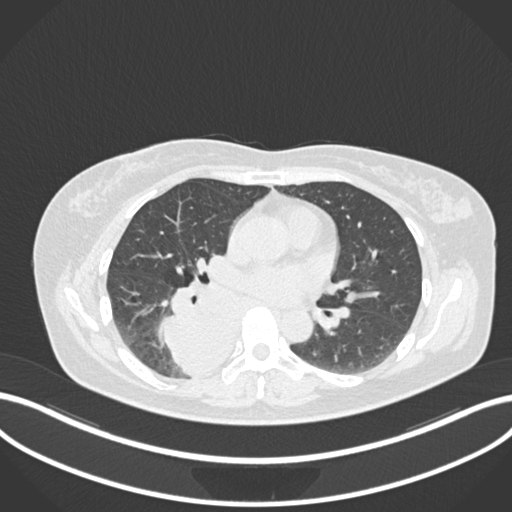
Chest CT, one axial slice; reconstruction kernel B30f; 120 kVp; lung window (W 1500 / L -600 HU); 1 mm slice thickness; 512 × 512 image matrix, field of view 400 × 400 mm. Patient: female, 54 years. Case-level facts recorded for this patient, not image findings: clinical TNM (as recorded): T4 N0 M0.
Outlined on this slice (rectangle marked by the reading radiologist):
- lung tumour (recorded histology: adenocarcinoma): bounding box [x1, y1, x2, y2] px = [152, 270, 241, 378]